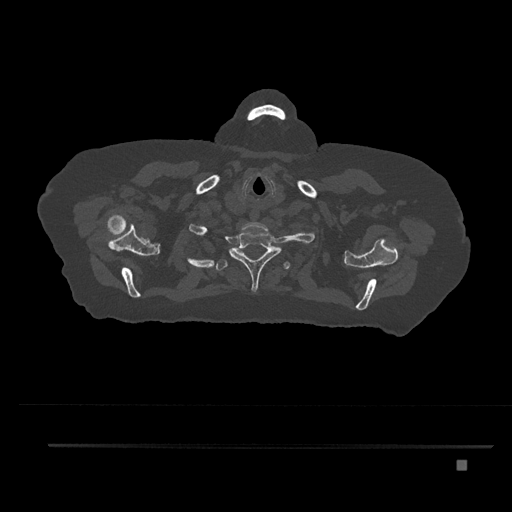
CT including the spine, one axial slice; slice 695 of 797 in the series (ordered by position); reconstruction kernel Br40s/3; 120 kVp; bone window (W 1800 / L 400 HU); 0.5 mm slice thickness; 512 × 512 image matrix, field of view 437 × 437 mm. Patient: female, 76 years. From the clinical record (not read from this slice): primary cancer: lung.
Structures marked on this image (semi-automatic segmentation, software-assisted and operator-edited):
- T1 vertebra: box from (x=229, y=229) to (x=281, y=292) px
- T2 vertebra: (x=207, y=248)–(x=290, y=271)